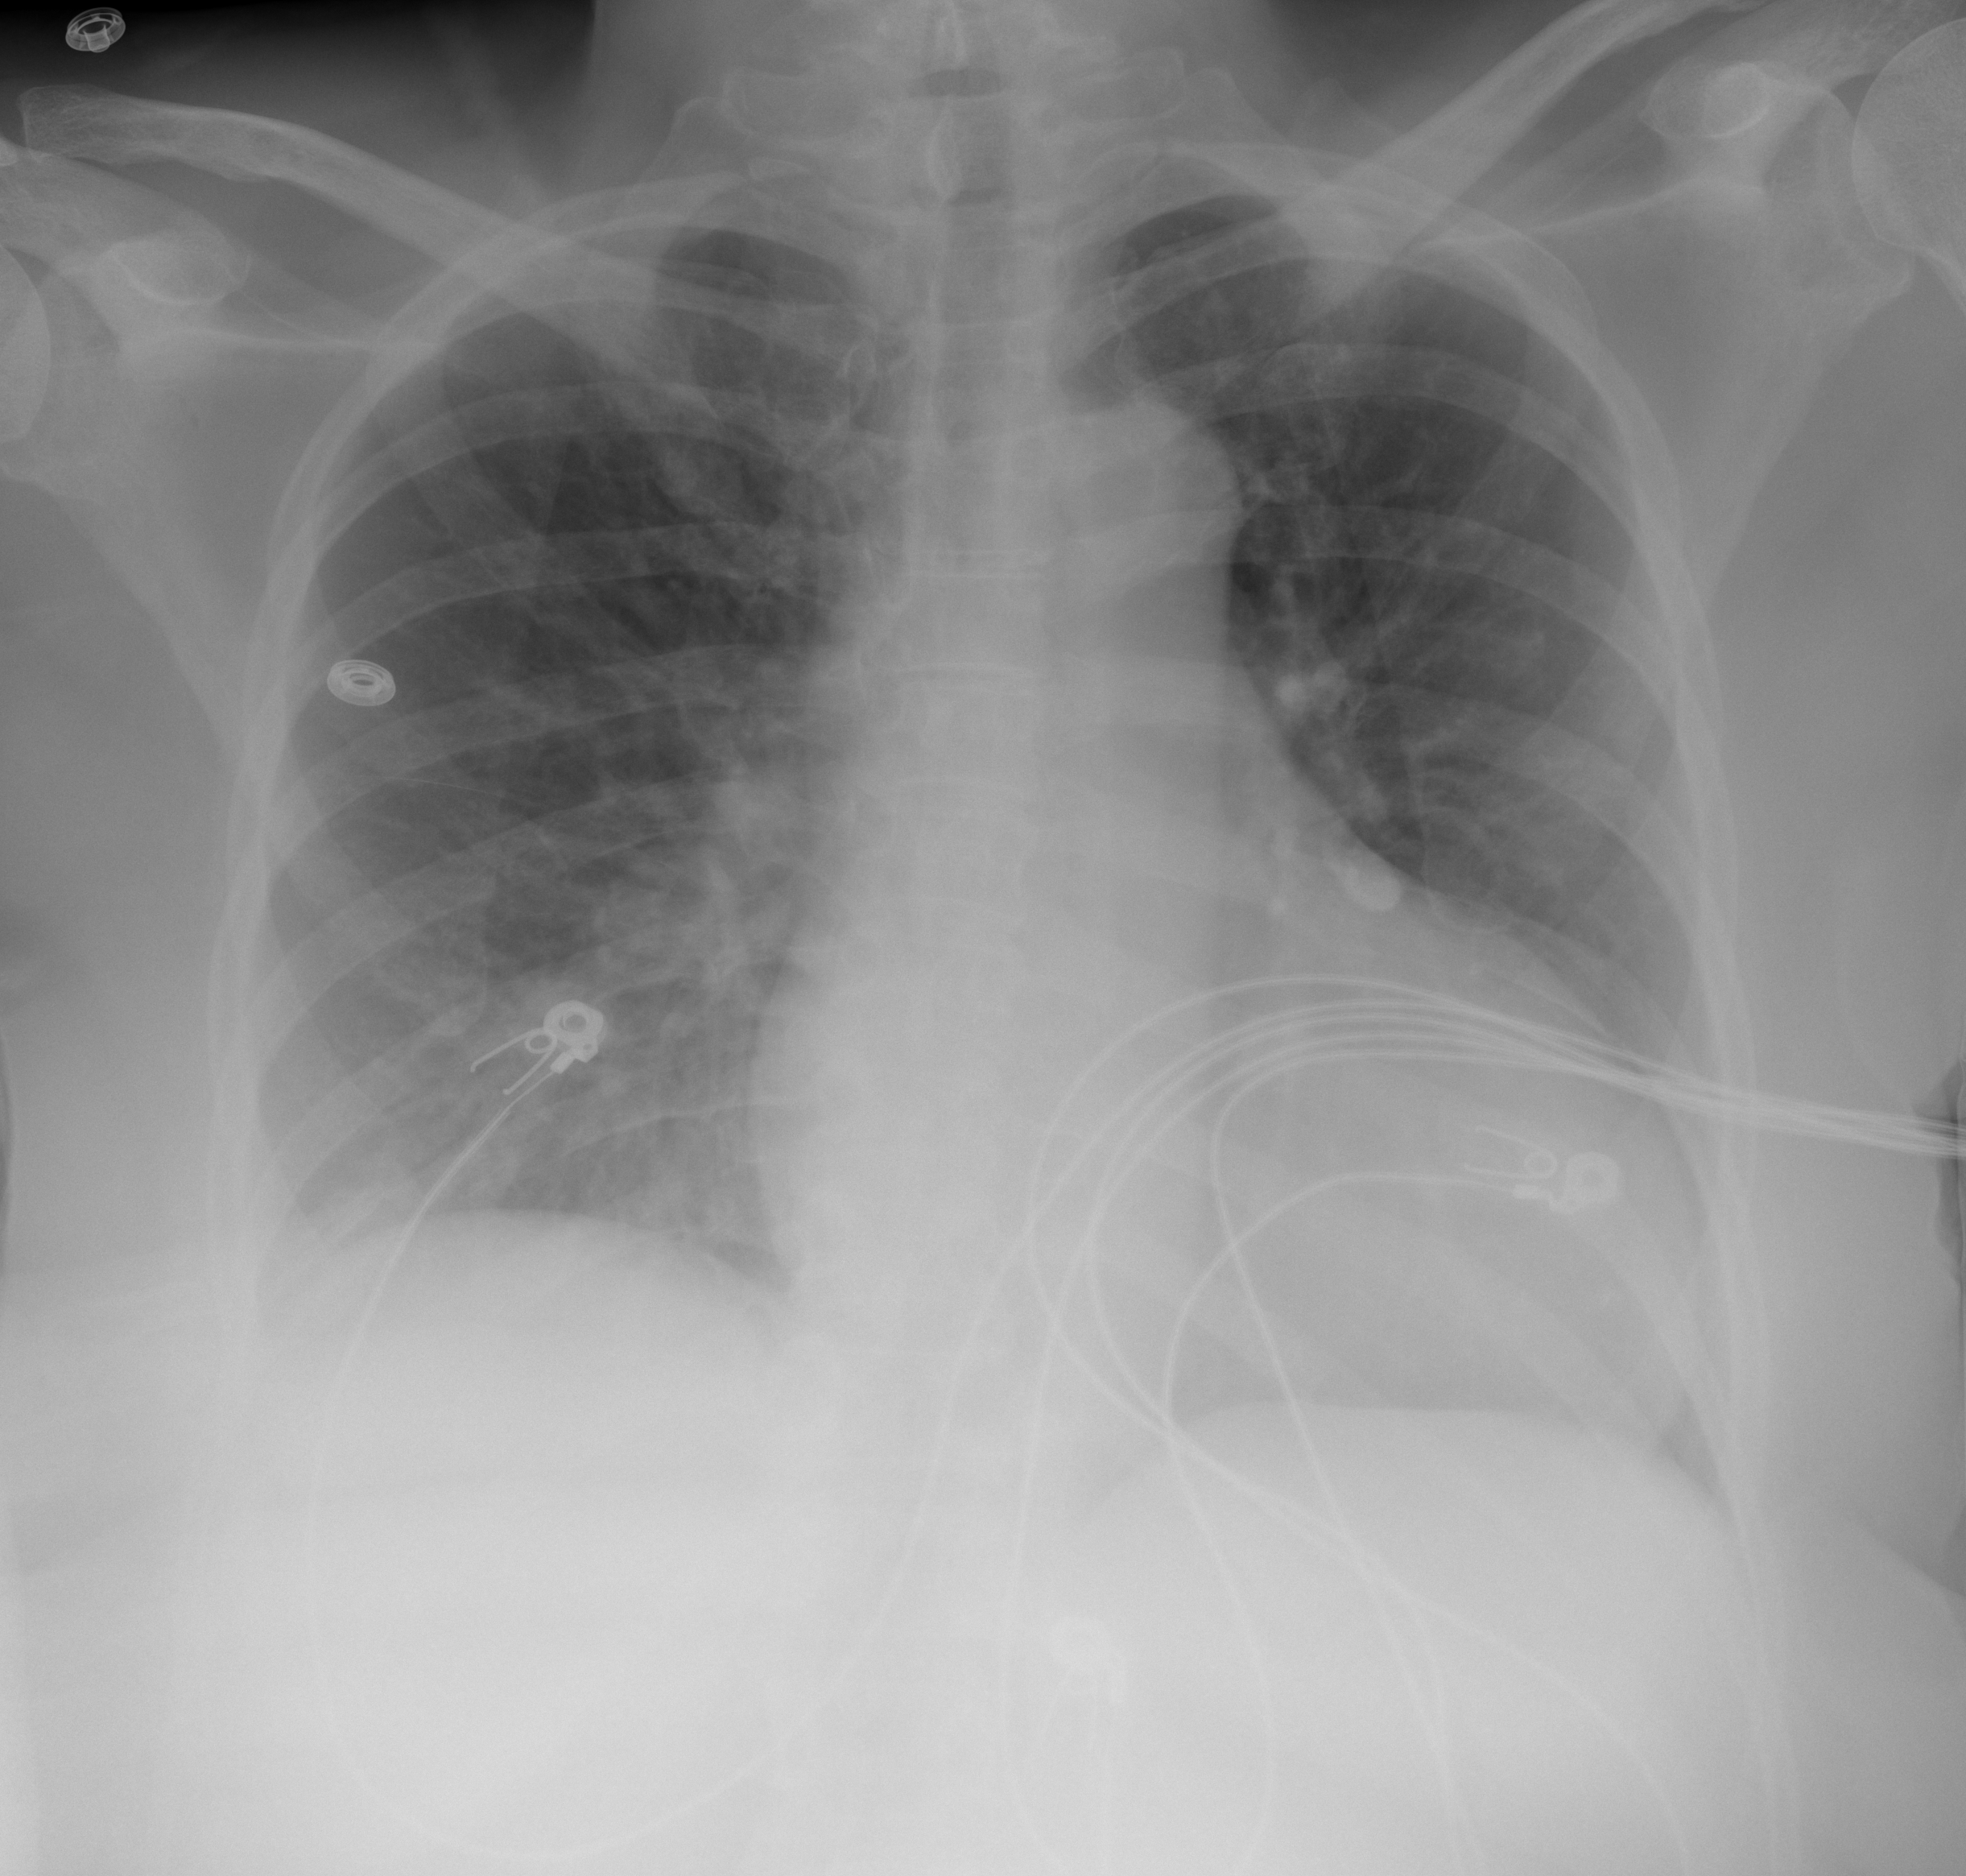
Portable chest radiograph, AP projection. Female patient, age 51 years; imaged 0 days after the COVID-19 diagnosis.
Radiologist's key findings for this exam: Interval development of right infrahilar opacities.